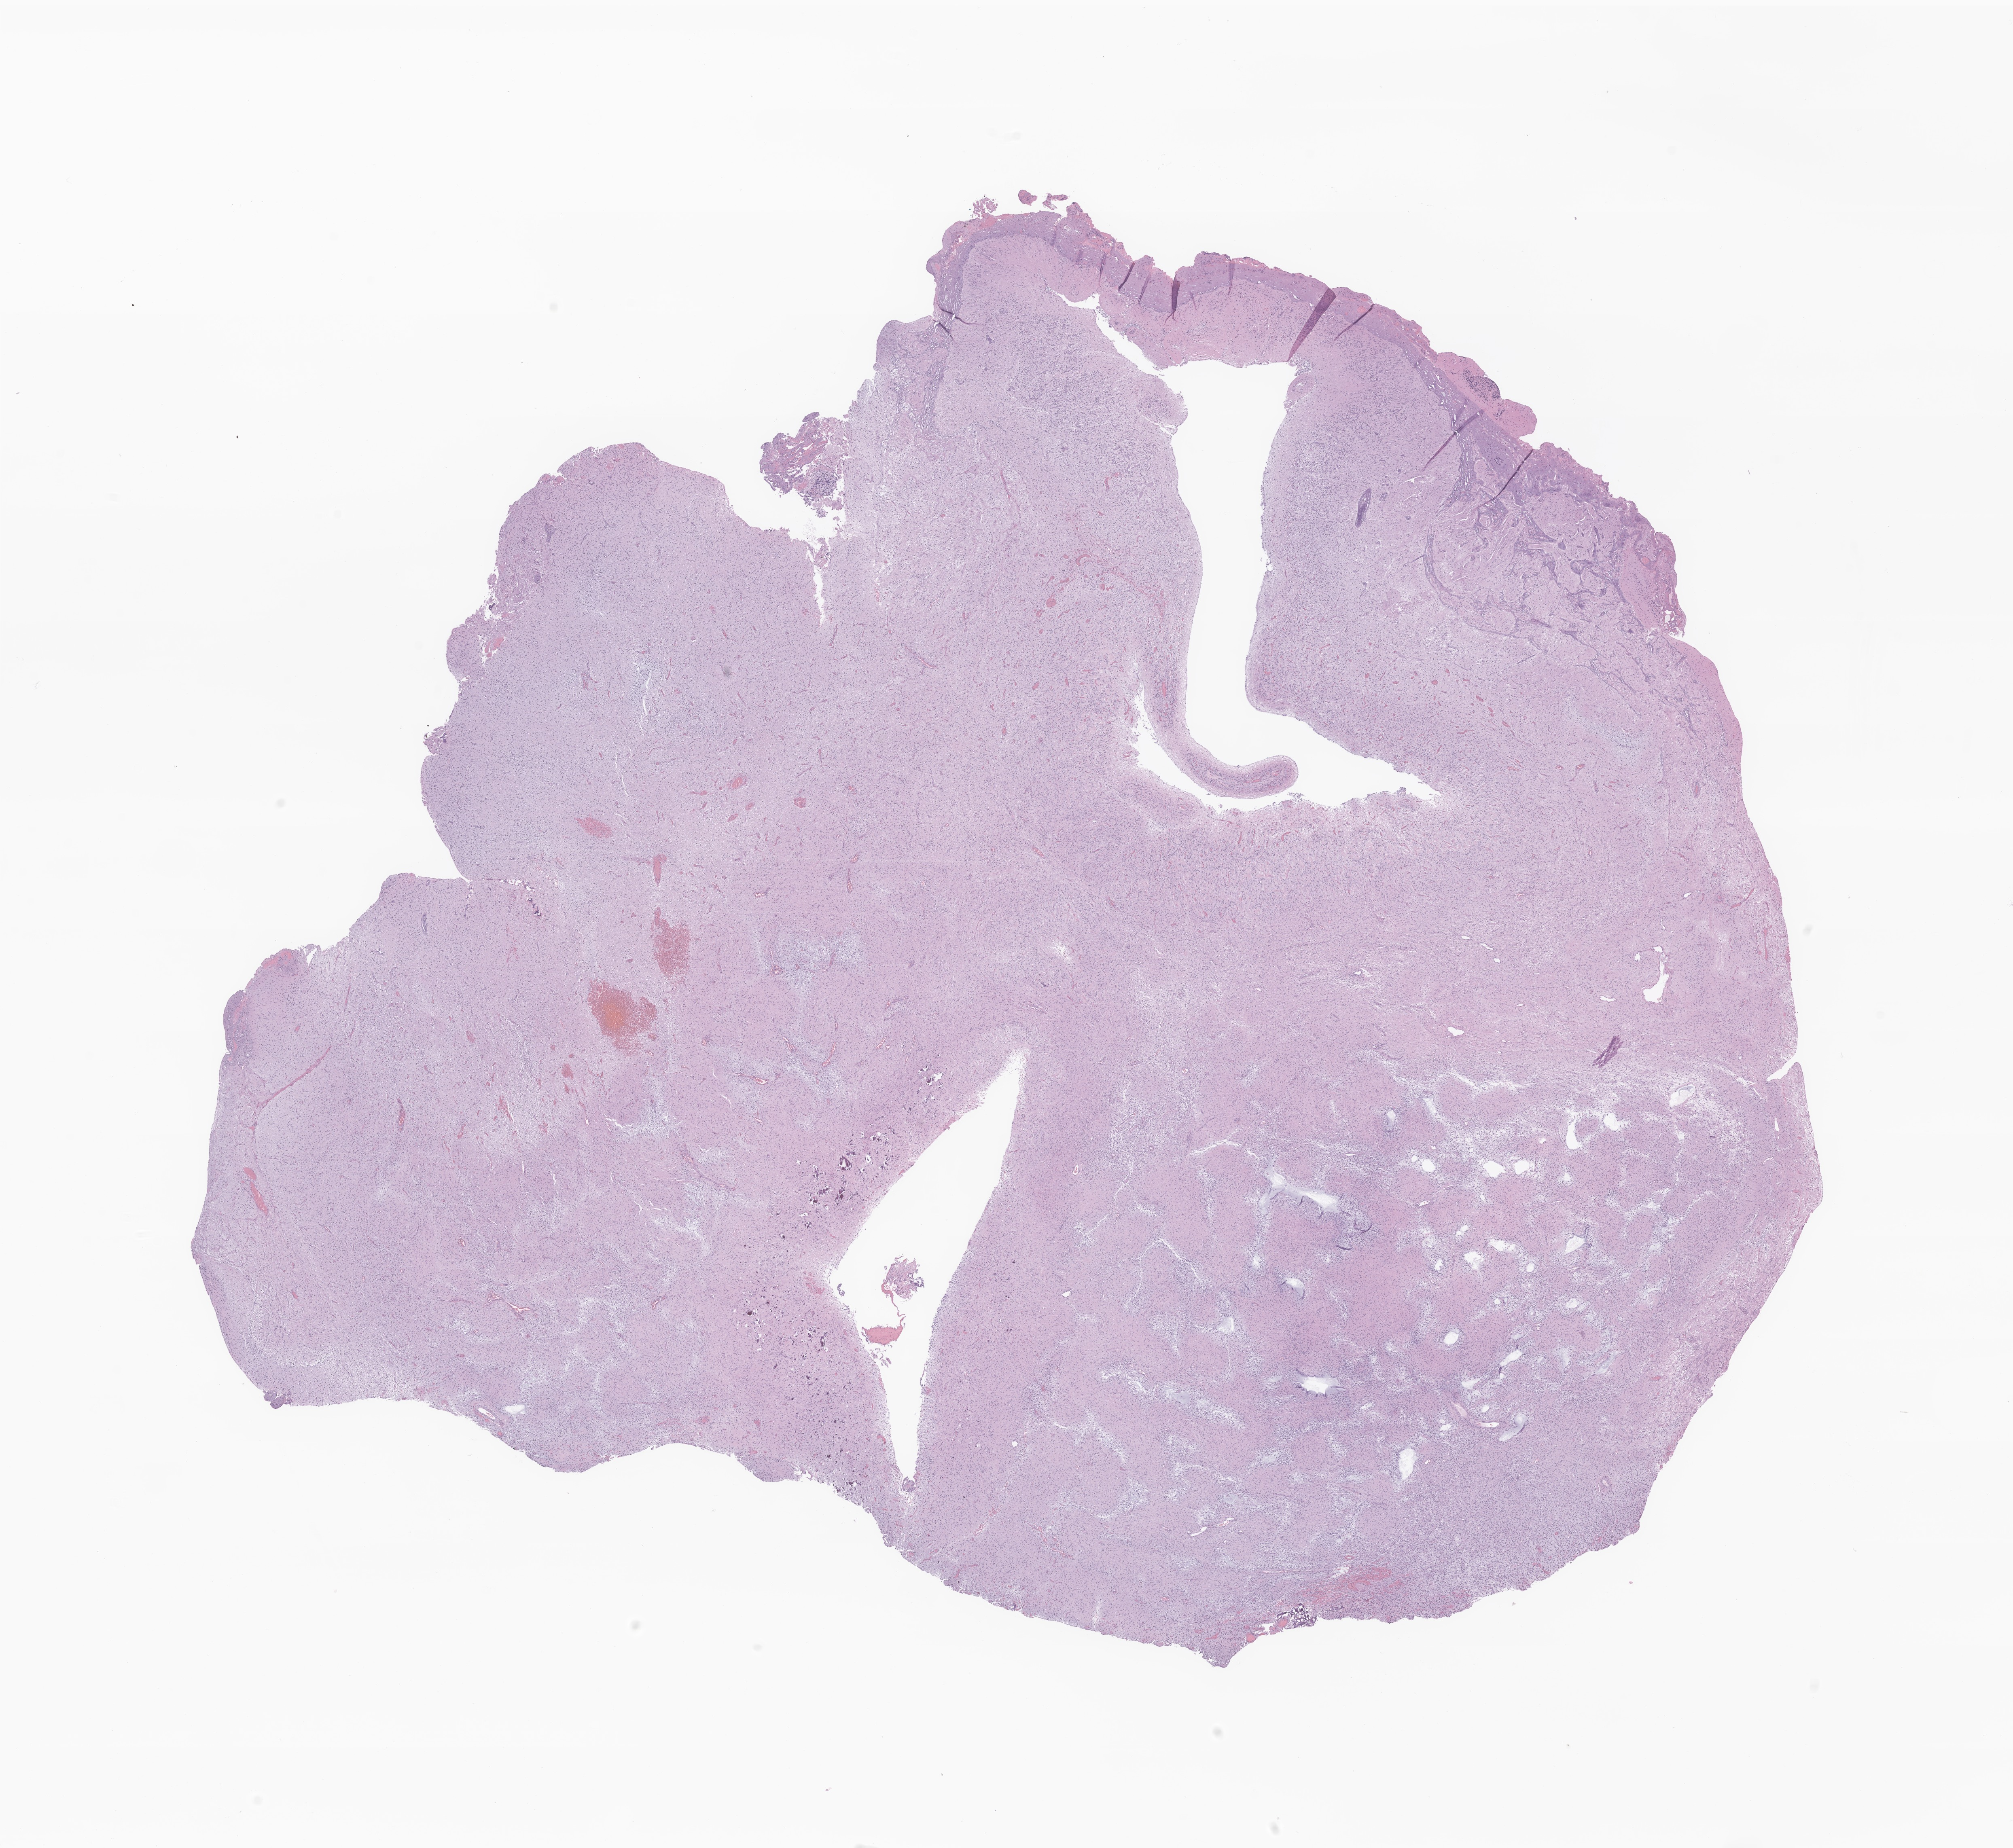
Digitized H&E-stained section of tumor tissue from the cerebellum, shown as a low-resolution overview of the whole scanned area (about 21.0 x 19.3 mm); formalin-fixed, paraffin-embedded (FFPE) tissue. Patient: female, age 80 months (6 years 8 months).
Recorded diagnosis: Pilocytic astrocytoma.